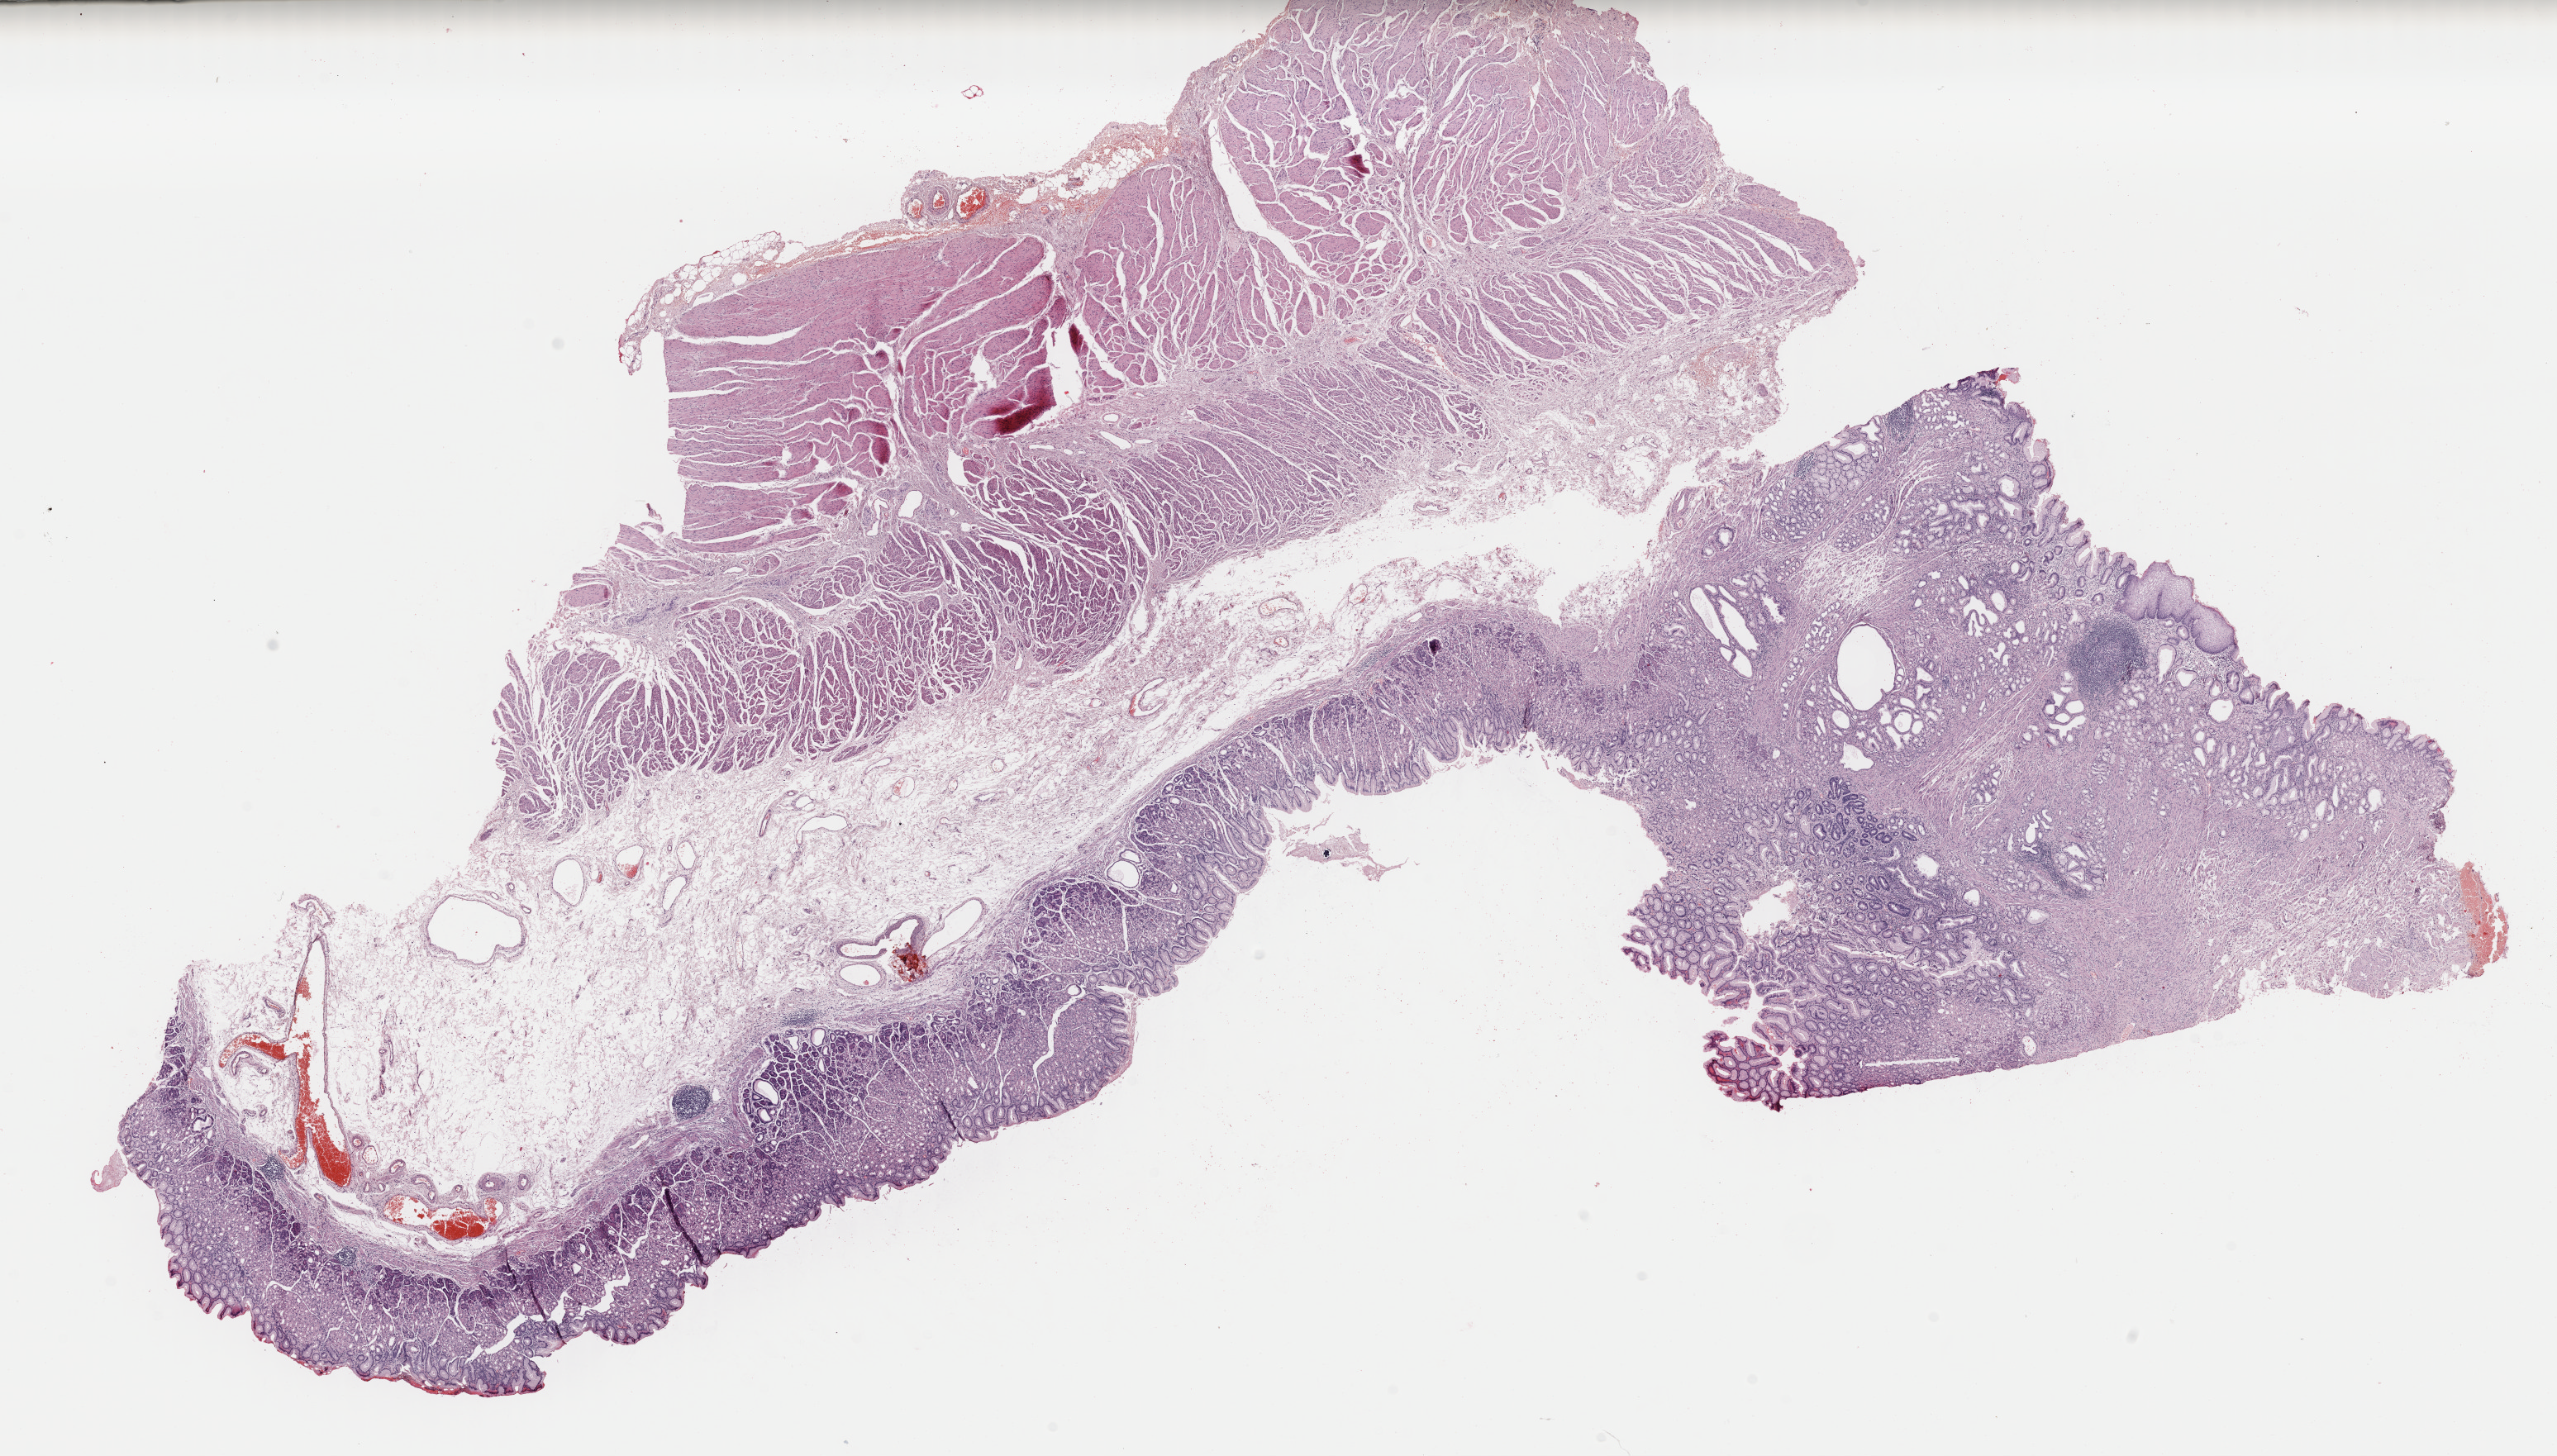
Digitized H&E-stained tissue section (whole slide), a low-resolution overview of the entire scanned area, about 24.4 x 13.9 mm (acquisition: 40x scan); FFPE section; stomach, primary tumour sample. Patient: male, age at initial diagnosis 72 years. Histologic grade: G3 (poorly differentiated).
Lymph nodes positive (case pathology): 13 of 16 examined. Diagnosis: Adenocarcinoma, NOS (gastric antrum). AJCC pathologic stage: IIIA. TNM: T2 N3a M0.